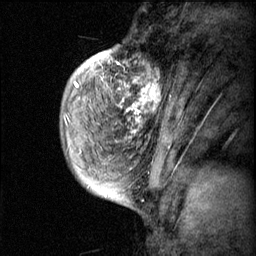
Breast MRI (dynamic contrast-enhanced), one sagittal slice. Slice 13 of 60 in the series (ordered by position). Dynamic contrast-enhanced series, image 2 of 3 at this slice position (ordered by acquisition). 1.5 T. TE 4.2 ms, TR 11.1 ms. 2 mm slice thickness. 256 × 256 image matrix, field of view 180 × 180 mm. Female patient, age 50 years.
Outlined on this slice (semi-automatic segmentation, software-assisted and operator-edited):
- analysis volume of interest (the breast-tissue region the enhancement analysis was run in; not a lesion): bounding box <82,56,168,143> (left, top, right, bottom; pixels)
- tumour enhancement mask (voxels above the 70 % enhancement threshold inside the analysis volume of interest): <82,56,166,143>